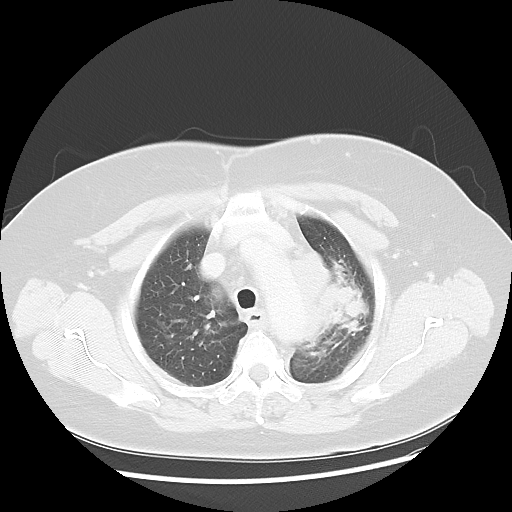
Chest CT, one axial slice. Position 38 of 49 along the scan axis. Reconstruction kernel LUNG. 120 kVp. Lung window (W 1500 / L -600 HU). 5 mm slice thickness. 512 × 512 image matrix, field of view 374 × 374 mm. Female patient, age 58 years. From the clinical record (not read from this slice): clinical TNM (as recorded): T4 N3 M0; histopathological grade: G3.
Structures marked on this image (rectangle marked by the reading radiologist):
- lung tumour (recorded histology: small cell carcinoma): bounding box <290,240,382,356> (left, top, right, bottom; pixels)